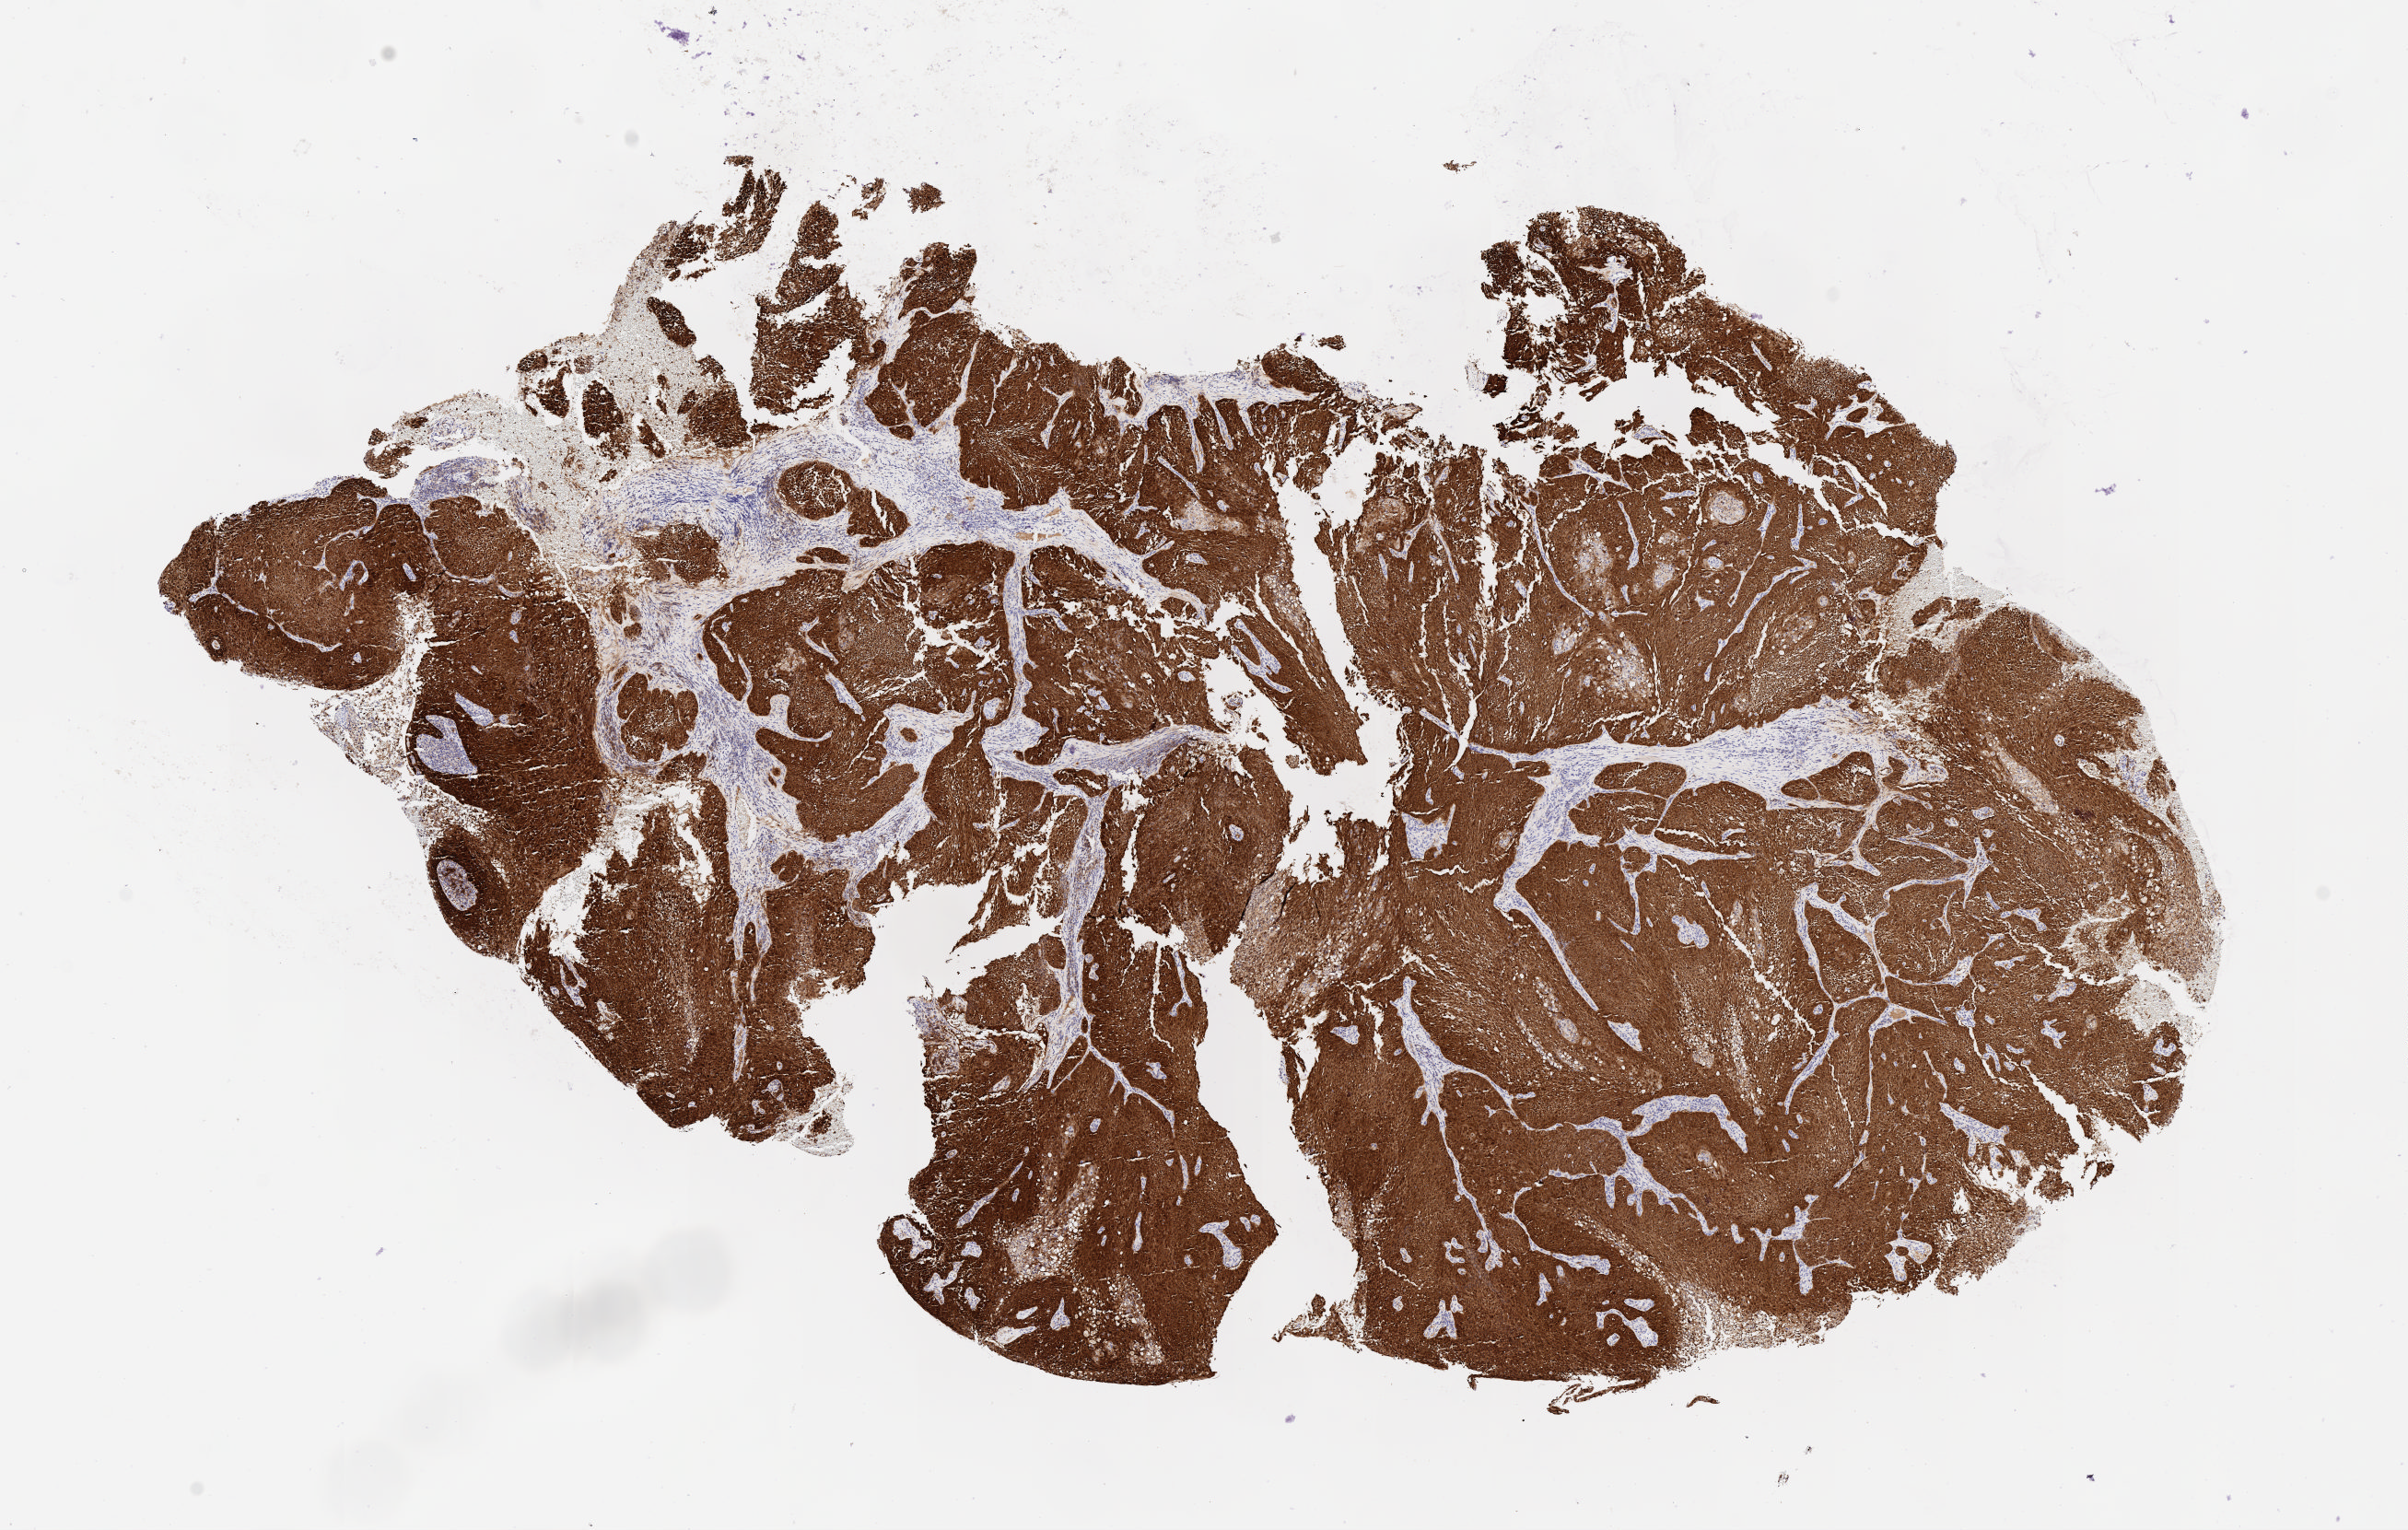
Whole-slide image, immunohistochemical stain for p16 (p16INK4a) — whole scanned area (about 10.6 x 6.7 mm) shown as a low-resolution overview. Tumor tissue. Anatomic site: cervix. Patient female; 45 years old.
Diagnosis: Squamous cell carcinoma, keratinizing, NOS.